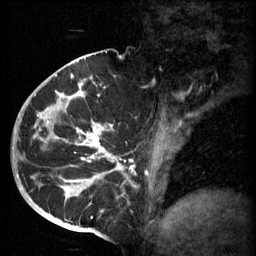
Breast MRI (dynamic contrast-enhanced), one sagittal slice. Position 34 of 60 along the scan axis. 3 images stored at this slice position (order not interpretable as contrast timing). 1.5 T. TE 4.2 ms, TR 11 ms. 2 mm slice thickness. 256 × 256 image matrix, field of view 200 × 200 mm. Patient: female, 51 years.
Annotated regions visible in this slice (semi-automatic segmentation, software-assisted and operator-edited):
- analysis volume of interest (the breast-tissue region the enhancement analysis was run in; not a lesion): bounding box (x1, y1, x2, y2) in pixels: (48, 82, 161, 197)
- tumour enhancement mask (voxels above the 70 % enhancement threshold inside the analysis volume of interest): (48, 92, 155, 191)